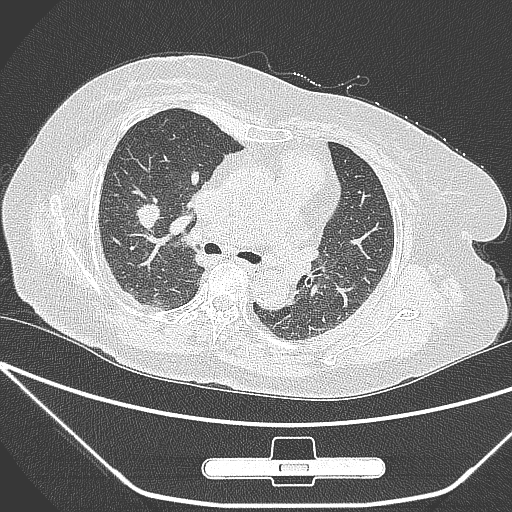
Chest CT, one axial slice. Position 162 of 245 along the scan axis. Lung window (W 1500 / L -600 HU). 1 mm slice thickness. 512 × 512 image matrix, field of view 365 × 365 mm. Female patient, age 65 years. From the clinical record (not read from this slice): clinical TNM (as recorded): T1c N0 M0.
Structures marked on this image (rectangle marked by the reading radiologist):
- lung tumour (recorded histology: adenocarcinoma): bounding box (x1, y1, x2, y2) in pixels: (128, 194, 163, 242)